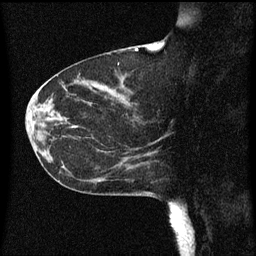
Breast MRI (dynamic contrast-enhanced), one sagittal slice; position 23 of 60 along the scan axis; dynamic contrast-enhanced series, image 2 of 3 at this slice position (ordered by acquisition); 1.5 T; TE 4.2 ms, TR 8 ms; 2 mm slice thickness; 256 × 256 image matrix, field of view 200 × 200 mm. Patient: female, 55 years.
Annotated regions visible in this slice (semi-automatically segmented with operator editing):
- analysis volume of interest (the breast-tissue region the enhancement analysis was run in; not a lesion): box from (x=46, y=124) to (x=151, y=183) px
- tumour enhancement mask (voxels above the 70 % enhancement threshold inside the analysis volume of interest): (x=134, y=150)–(x=143, y=165)